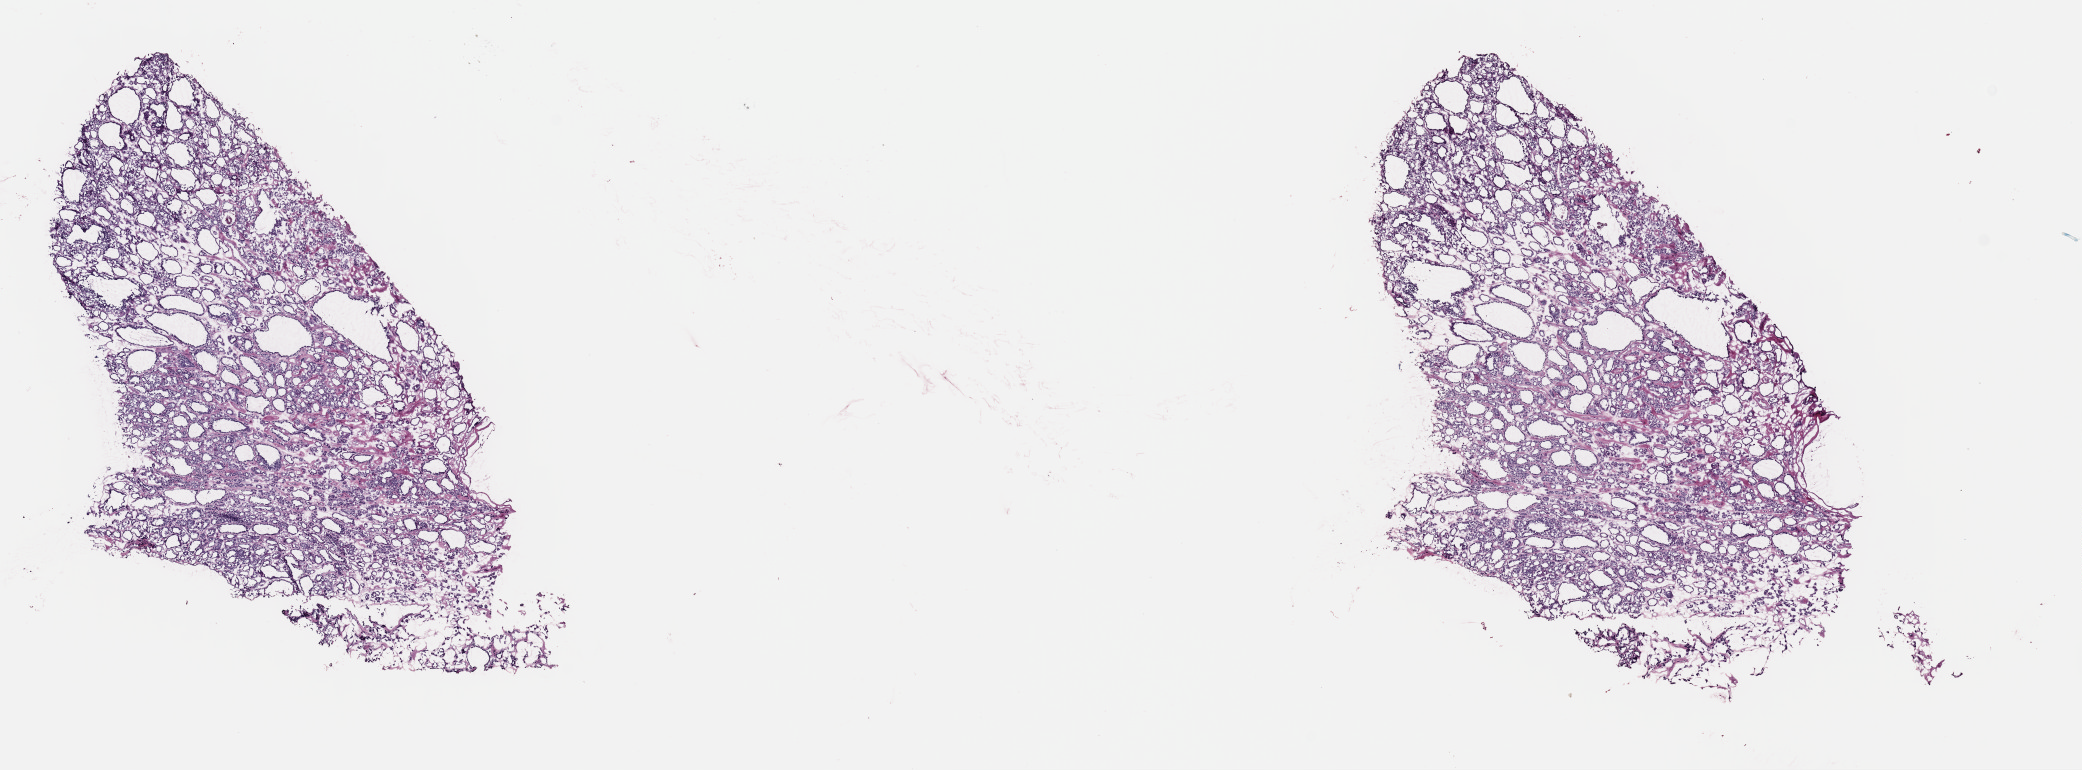
Whole-slide histology image, Hematoxylin and eosin (H&E) stained — low-resolution overview of the scanned area, about 16.4 x 6.1 mm. Frozen section from the top of the tissue portion. Sample: primary tumour, thyroid. Female patient; age at initial diagnosis 49 years. Pathologist review of this section (percent, as recorded): tumour cells 70%, tumour nuclei 100%, normal cells 0%, stromal cells 30%, necrosis 0%. Infiltration values recorded for this section: lymphocyte infiltration 0%, monocyte infiltration 1%, neutrophil infiltration 0%.
Diagnosis: Papillary carcinoma, follicular variant (thyroid gland). Laterality: left. AJCC pathologic stage: I (7th edition).